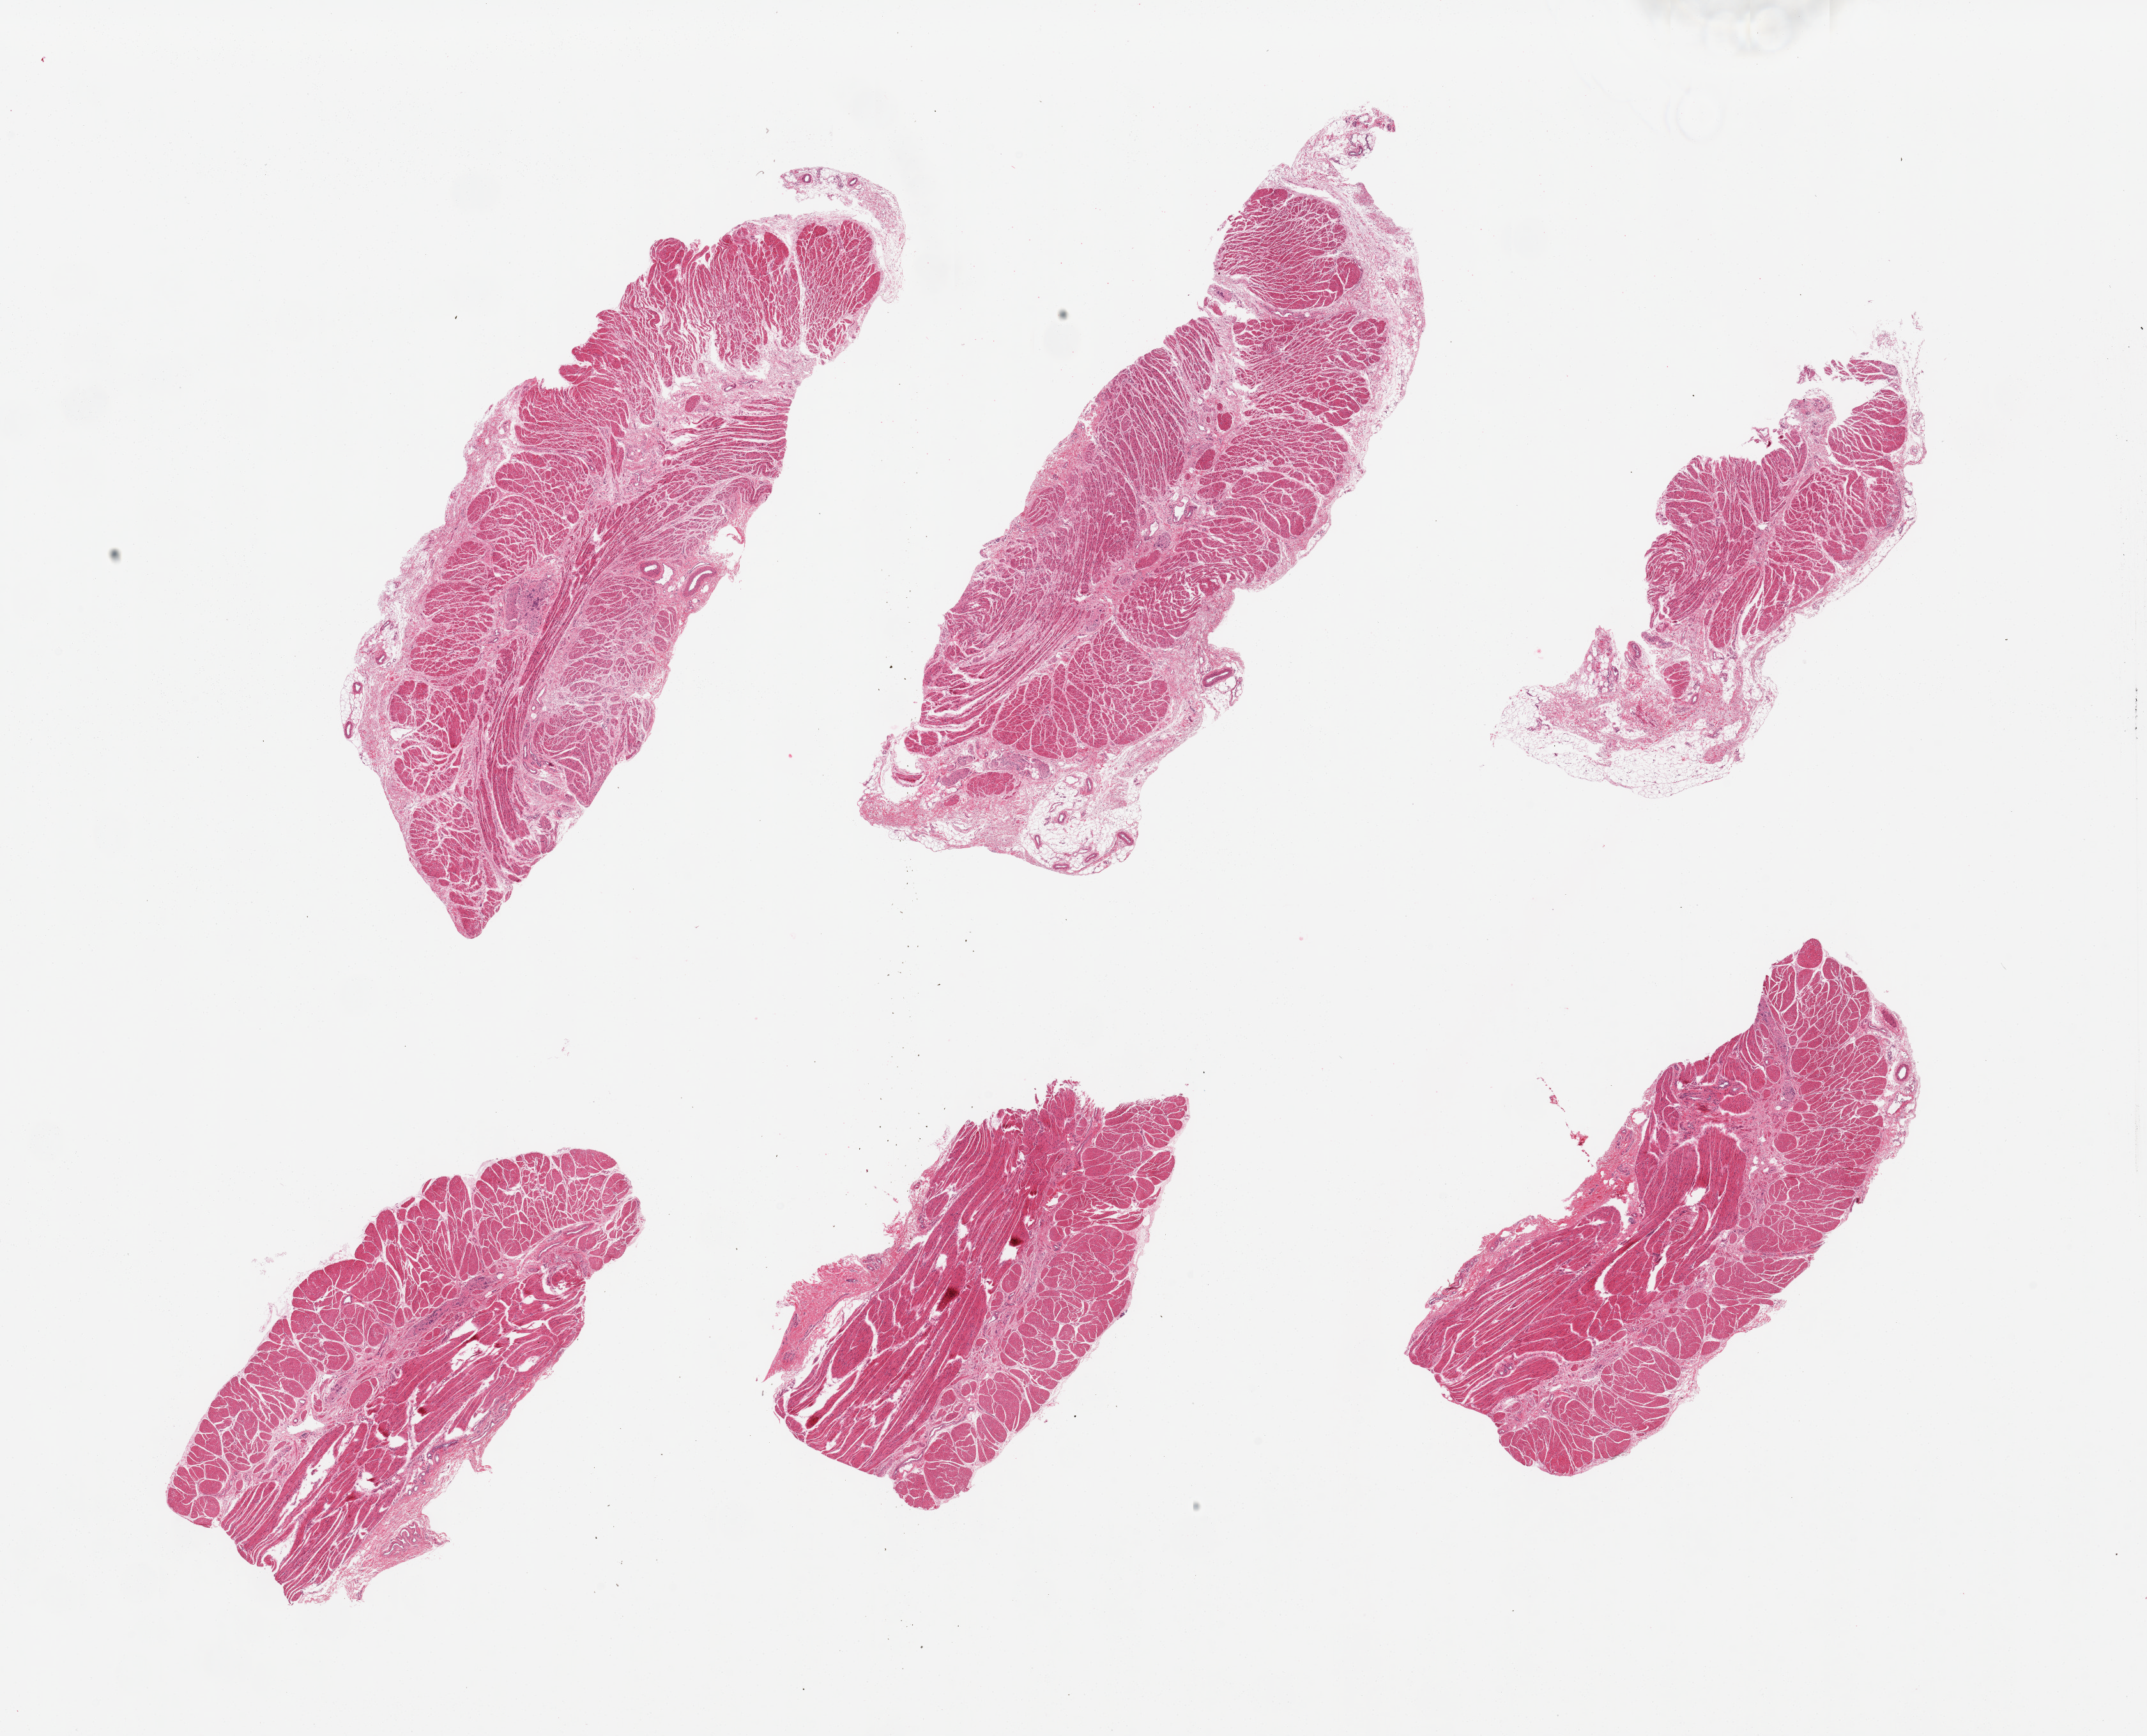
Whole-slide image, haematoxylin and eosin stain — low-resolution overview of the scanned area, about 26.6 x 21.5 mm (slide scanned at 20x). PAXgene-fixed, paraffin-embedded tissue. Sampled site (target tissue): gastroesophageal junction. Tissue donor sample.
Pathologist's review note for this sample: 6 pieces; musscle with small amount of submucosal stroma.